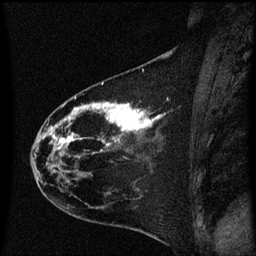
Breast MRI (dynamic contrast-enhanced), one sagittal slice. Position 26 of 60 along the scan axis. Dynamic contrast-enhanced series, image 2 of 3 at this slice position (ordered by acquisition). 1.5 T. TE 4.2 ms, TR 8.4 ms. 256 × 256 image matrix, field of view 200 × 200 mm. Patient: female, 35 years. From the clinical record (not read from this slice): setting: breast cancer imaged before/during neoadjuvant chemotherapy; receptor status: HER2-positive.
Outlined on this slice (semi-automatically segmented with operator editing):
- analysis volume of interest (the breast-tissue region the enhancement analysis was run in; not a lesion): bounding box <30,68,174,173> (left, top, right, bottom; pixels)
- tumour enhancement mask (voxels above the 70 % enhancement threshold inside the analysis volume of interest): <50,104,163,165>